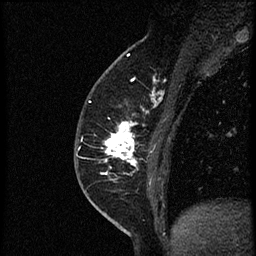
Breast MRI (dynamic contrast-enhanced), one sagittal slice; dynamic contrast-enhanced study with each time point stored as its own series, time point 2 of 4 at this slice position (early post-contrast, ordered by acquisition time); 1.5 T; TE 4.2 ms, TR 18.9 ms; 2 mm slice thickness; 256 × 256 image matrix, field of view 200 × 200 mm. Female patient. Case-level facts recorded for this patient, not image findings: setting: breast cancer imaged before/during neoadjuvant chemotherapy; receptor status: HER2-positive.
Annotated regions visible in this slice (semi-automatically segmented with operator editing):
- analysis volume of interest (the breast-tissue region the enhancement analysis was run in; not a lesion): bounding box (x1, y1, x2, y2) in pixels: (96, 85, 174, 189)
- tumour enhancement mask (voxels above the 100 % enhancement threshold inside the analysis volume of interest): (104, 98, 163, 175)